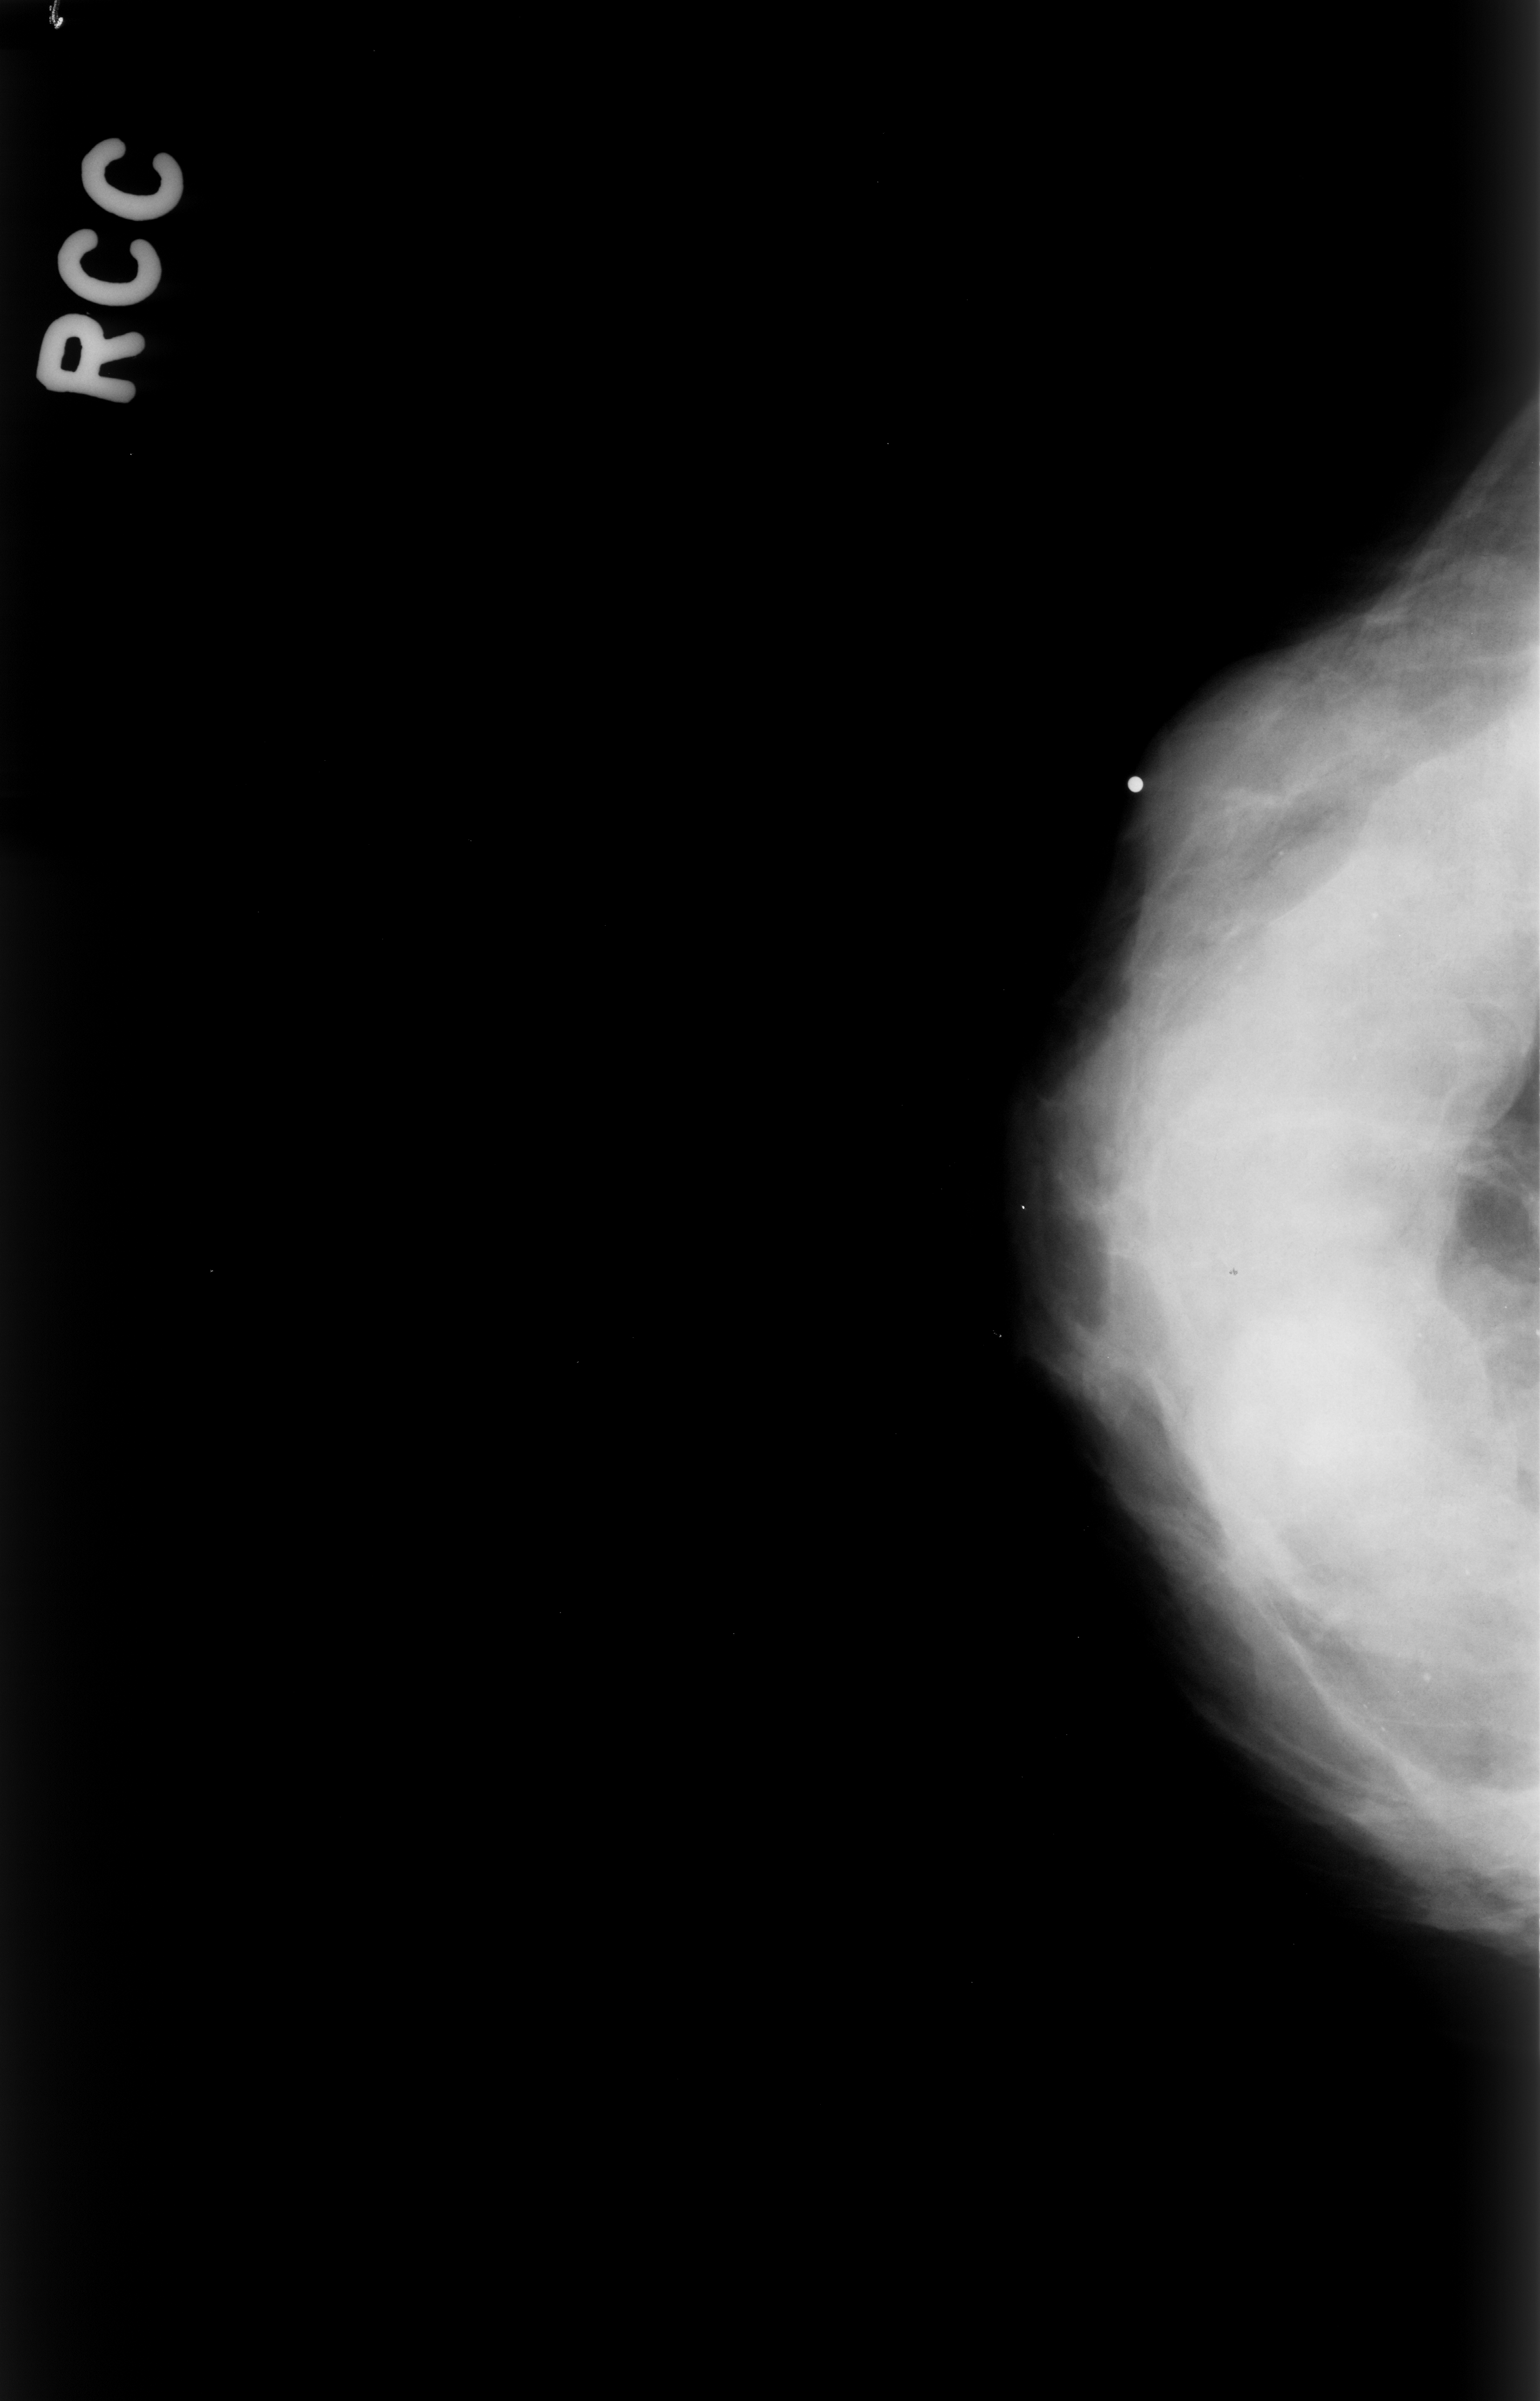
Mammogram (digitized film); right breast; CC view; breast composition: extremely dense (BI-RADS density category 4 of 4); 1540 × 2401 image matrix.
Expert-marked regions of interest on this film, with their recorded descriptors:
- calcifications, morphology punctate, distribution diffusely scattered; BI-RADS assessment category 2; subtlety rating 4 on a 1 (subtle) to 5 (obvious) scale; pathology result (as recorded, not read from the image): benign: bounding box <1098,765,1537,1909> (left, top, right, bottom; pixels)